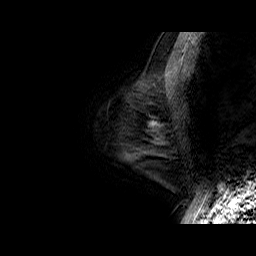
Breast MRI (dynamic contrast-enhanced), one sagittal slice. Slice 12 of 50 in the series (ordered by position). Dynamic contrast-enhanced series, time point 2 of 6 at this slice position (early post-contrast). 1.5 T. TE 6.5 ms, TR 32.9 ms. 4 mm slice thickness. 256 × 256 image matrix, field of view 200 × 200 mm. Female patient. From the clinical record (not read from this slice): setting: breast cancer imaged before/during neoadjuvant chemotherapy; receptor status: HR-positive, HER2-negative.
Structures marked on this image (semi-automatically segmented with operator editing):
- analysis volume of interest (the breast-tissue region the enhancement analysis was run in; not a lesion): bounding box [x1, y1, x2, y2] px = [138, 75, 179, 146]
- tumour enhancement mask (voxels above the 100 % enhancement threshold inside the analysis volume of interest): [150, 123, 157, 127]